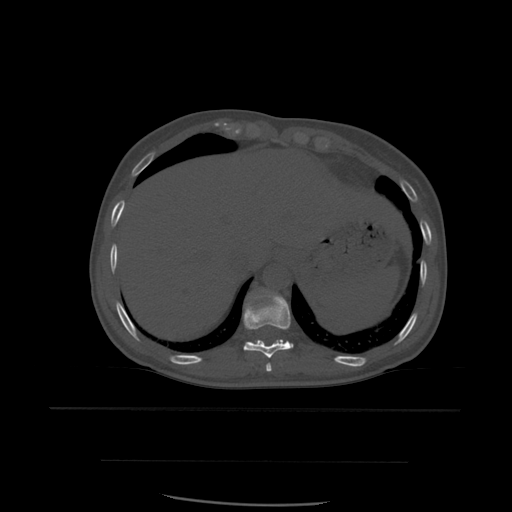
CT including the spine, one axial slice; position 313 of 574 along the scan axis; bone window (W 1800 / L 400 HU); 1.25 mm slice thickness; 512 × 512 image matrix. Patient age 48 years. Case-level facts recorded for this patient, not image findings: primary cancer: lung; vertebrae with lytic lesions (as recorded): T11.
Outlined on this slice (semi-automatic segmentation, software-assisted and operator-edited):
- T10 vertebra: bounding box <244,292,294,359> (left, top, right, bottom; pixels)
- T11 vertebra: <253,340,265,346>
- T9 vertebra: <266,363,272,372>